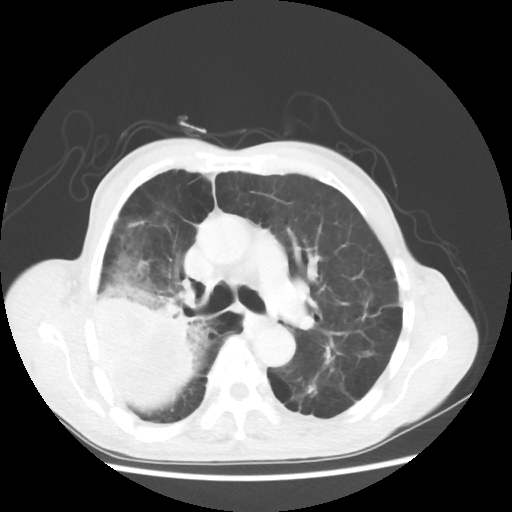
Chest CT, one axial slice. Position 34 of 58 along the scan axis. Reconstruction kernel STANDARD. 100 kVp. Lung window (W 1500 / L -600 HU). 5 mm slice thickness. 512 × 512 image matrix. Male patient, age 75 years. From the clinical record (not read from this slice): clinical TNM (as recorded): T4 N1 M1.
Annotated regions visible in this slice (rectangle marked by the reading radiologist):
- lung tumour (recorded histology: adenocarcinoma): box from (x=87, y=269) to (x=208, y=414) px